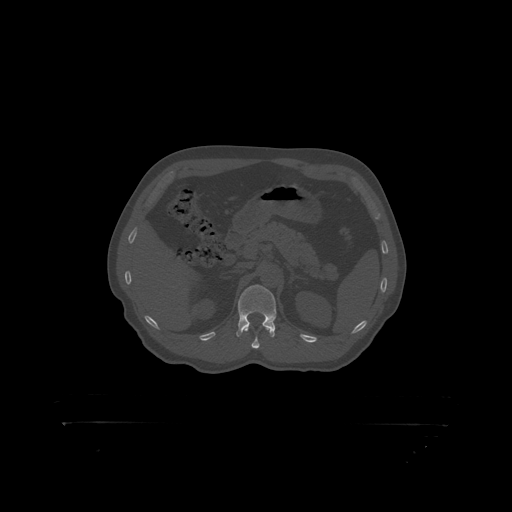
CT including the spine, one axial slice; position 334 of 399 along the scan axis; reconstruction kernel STANDARD; bone window (W 1800 / L 400 HU); 1.25 mm slice thickness; 512 × 512 image matrix, field of view 650 × 650 mm. Patient: male, 46 years. From the clinical record (not read from this slice): primary cancer: skin.
Outlined on this slice (semi-automatically segmented with operator editing):
- L1 vertebra: bounding box [x1, y1, x2, y2] px = [239, 285, 277, 319]